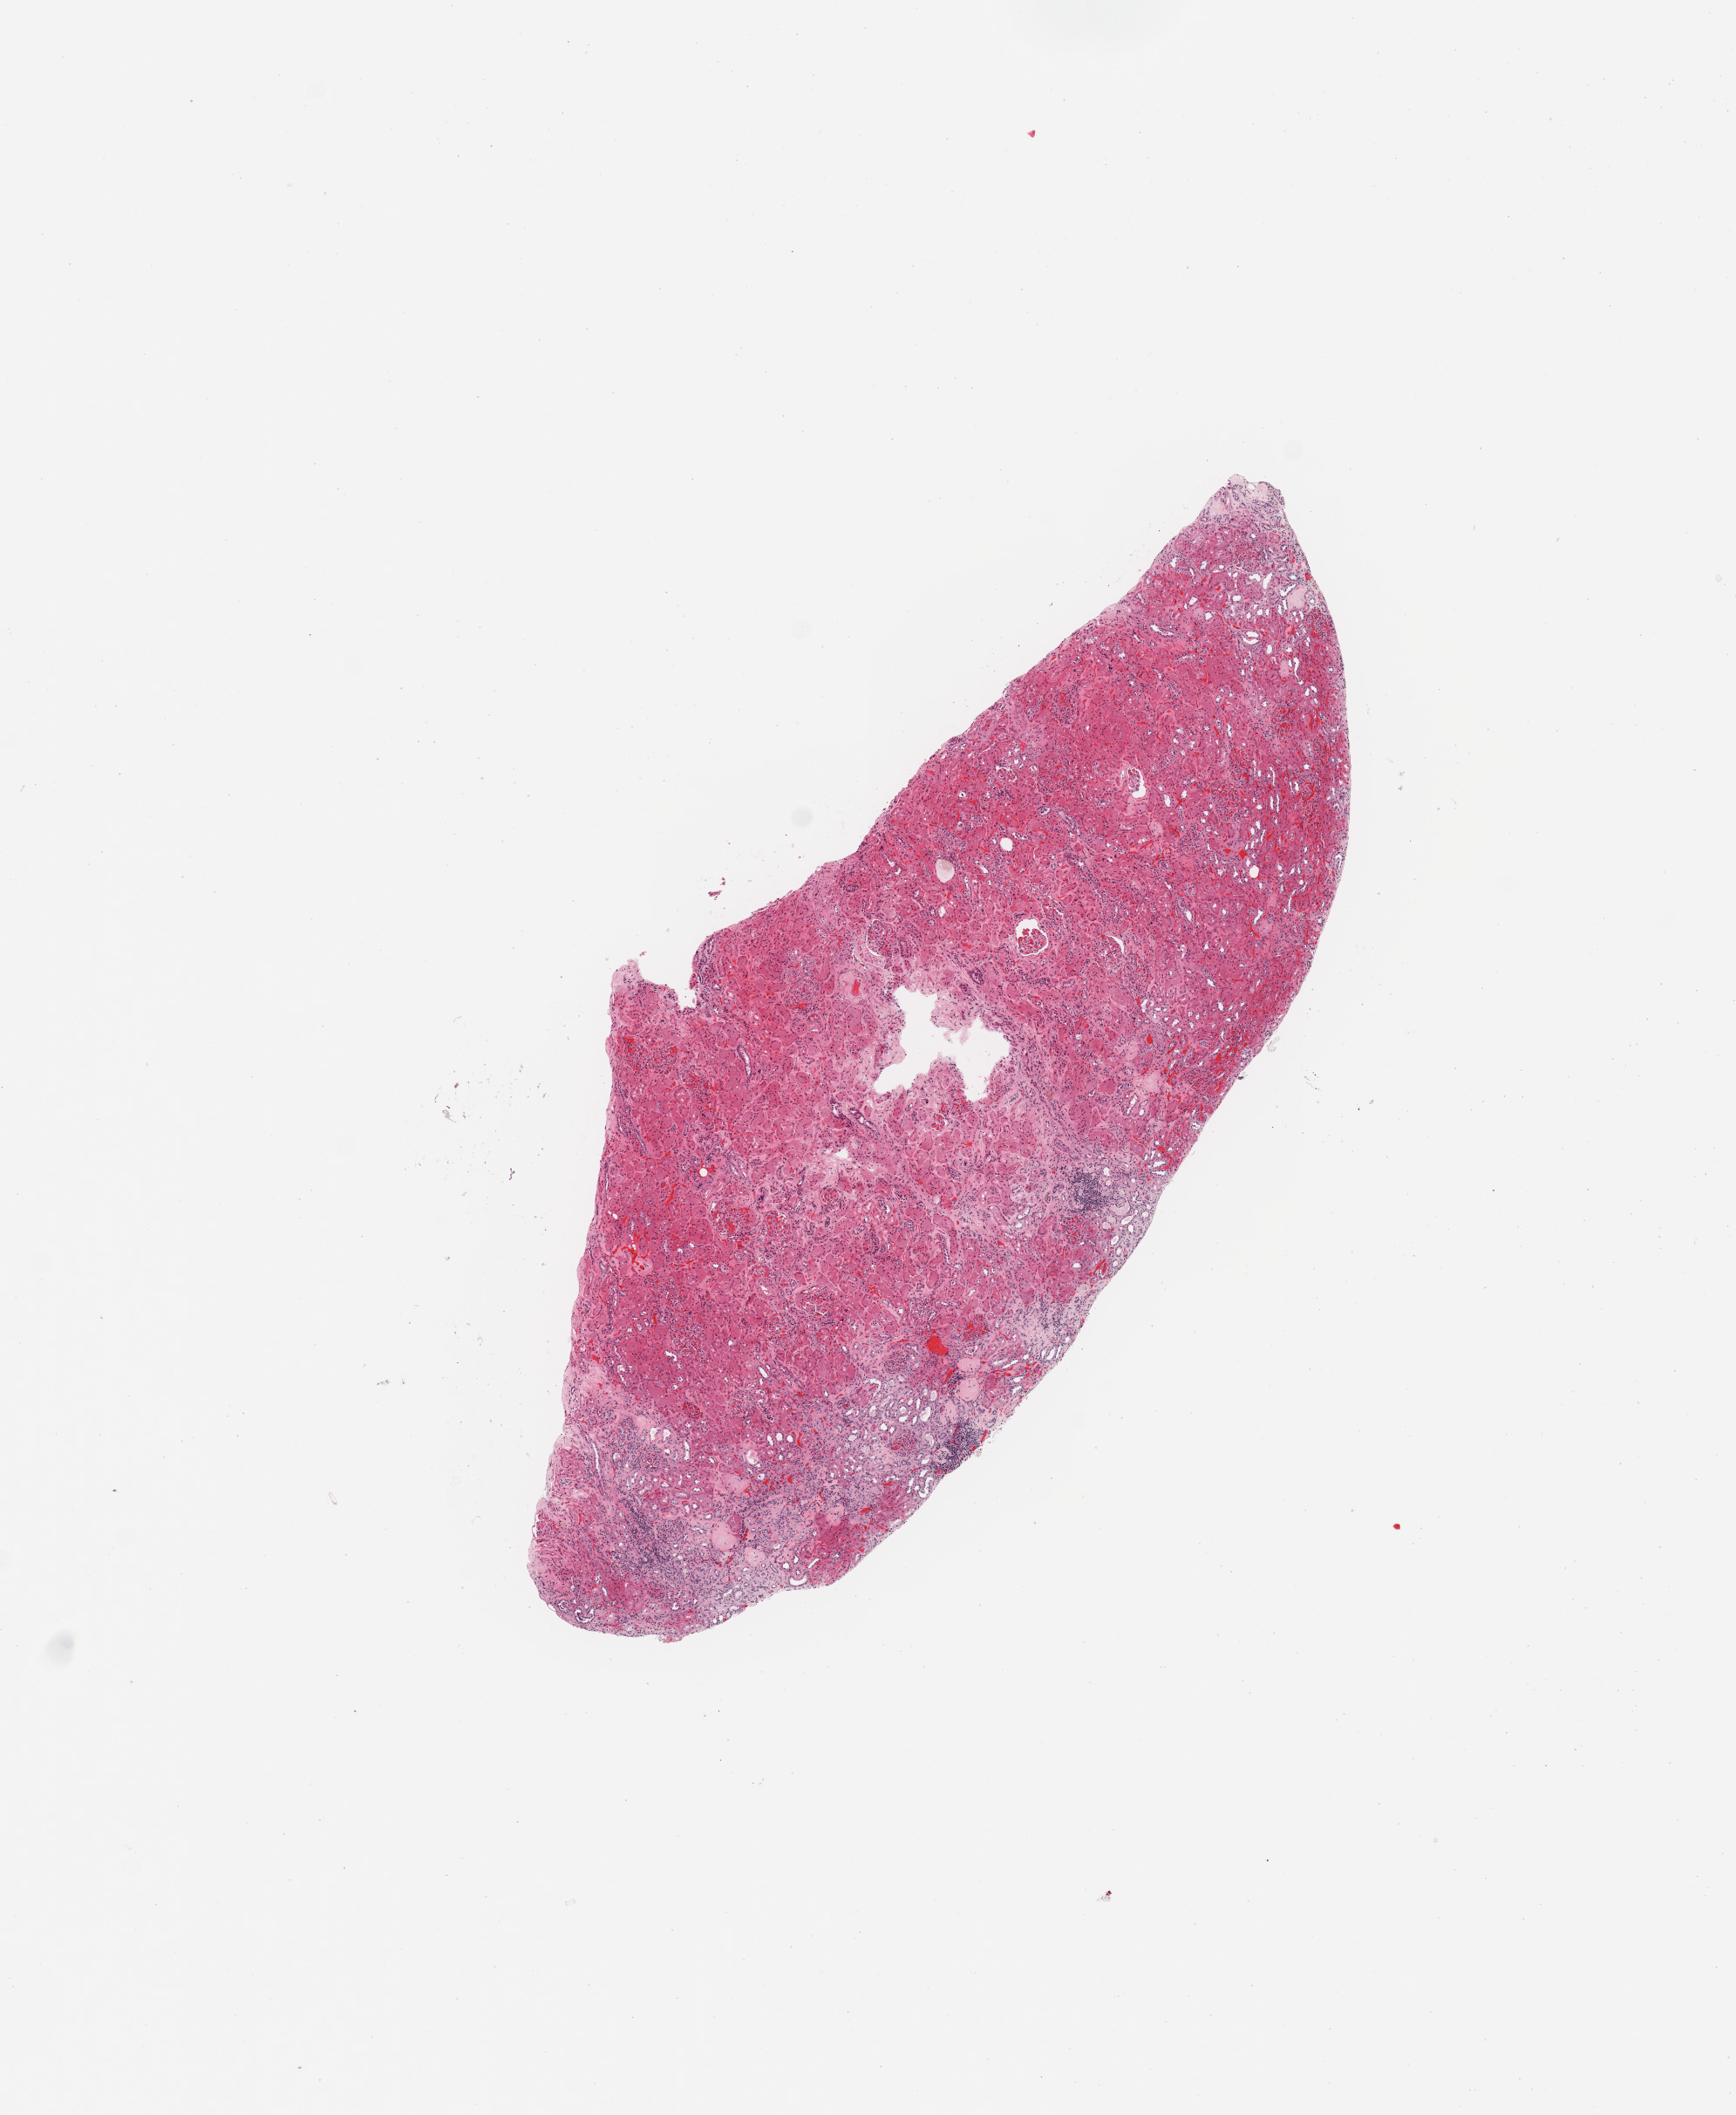
Digitized Hematoxylin and eosin (H&E) stained tissue section (whole slide), shown as a low-resolution overview of the whole scanned area (about 7.9 x 9.6 mm); normal (non-tumour) tissue sample, sampled site: kidney. Male, 85 y/o.
- this section: normal (non-tumour) tissue from the same patient
- patient diagnosis: Renal cell carcinoma, NOS